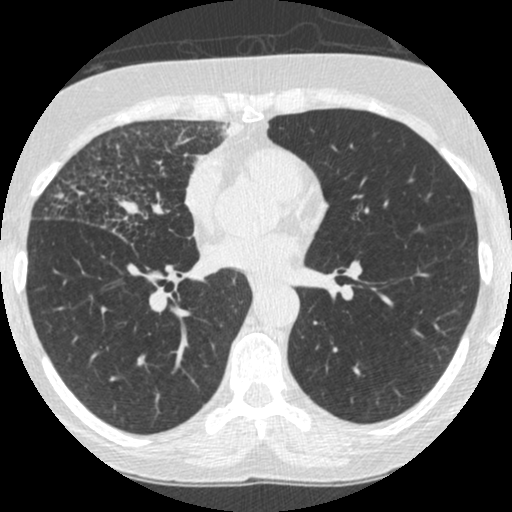
Low-dose screening chest CT, one axial slice; position 126 of 253 along the scan axis; reconstruction kernel STANDARD; 120 kVp; lung window (W 1500 / L -600 HU); 1.25 mm slice thickness; 512 × 512 image matrix.
Structures marked on this image (outlined manually by an expert reader):
- lesion 4 (tumor, upper lobe of right lung): bounding box <200,118,242,156> (left, top, right, bottom; pixels)